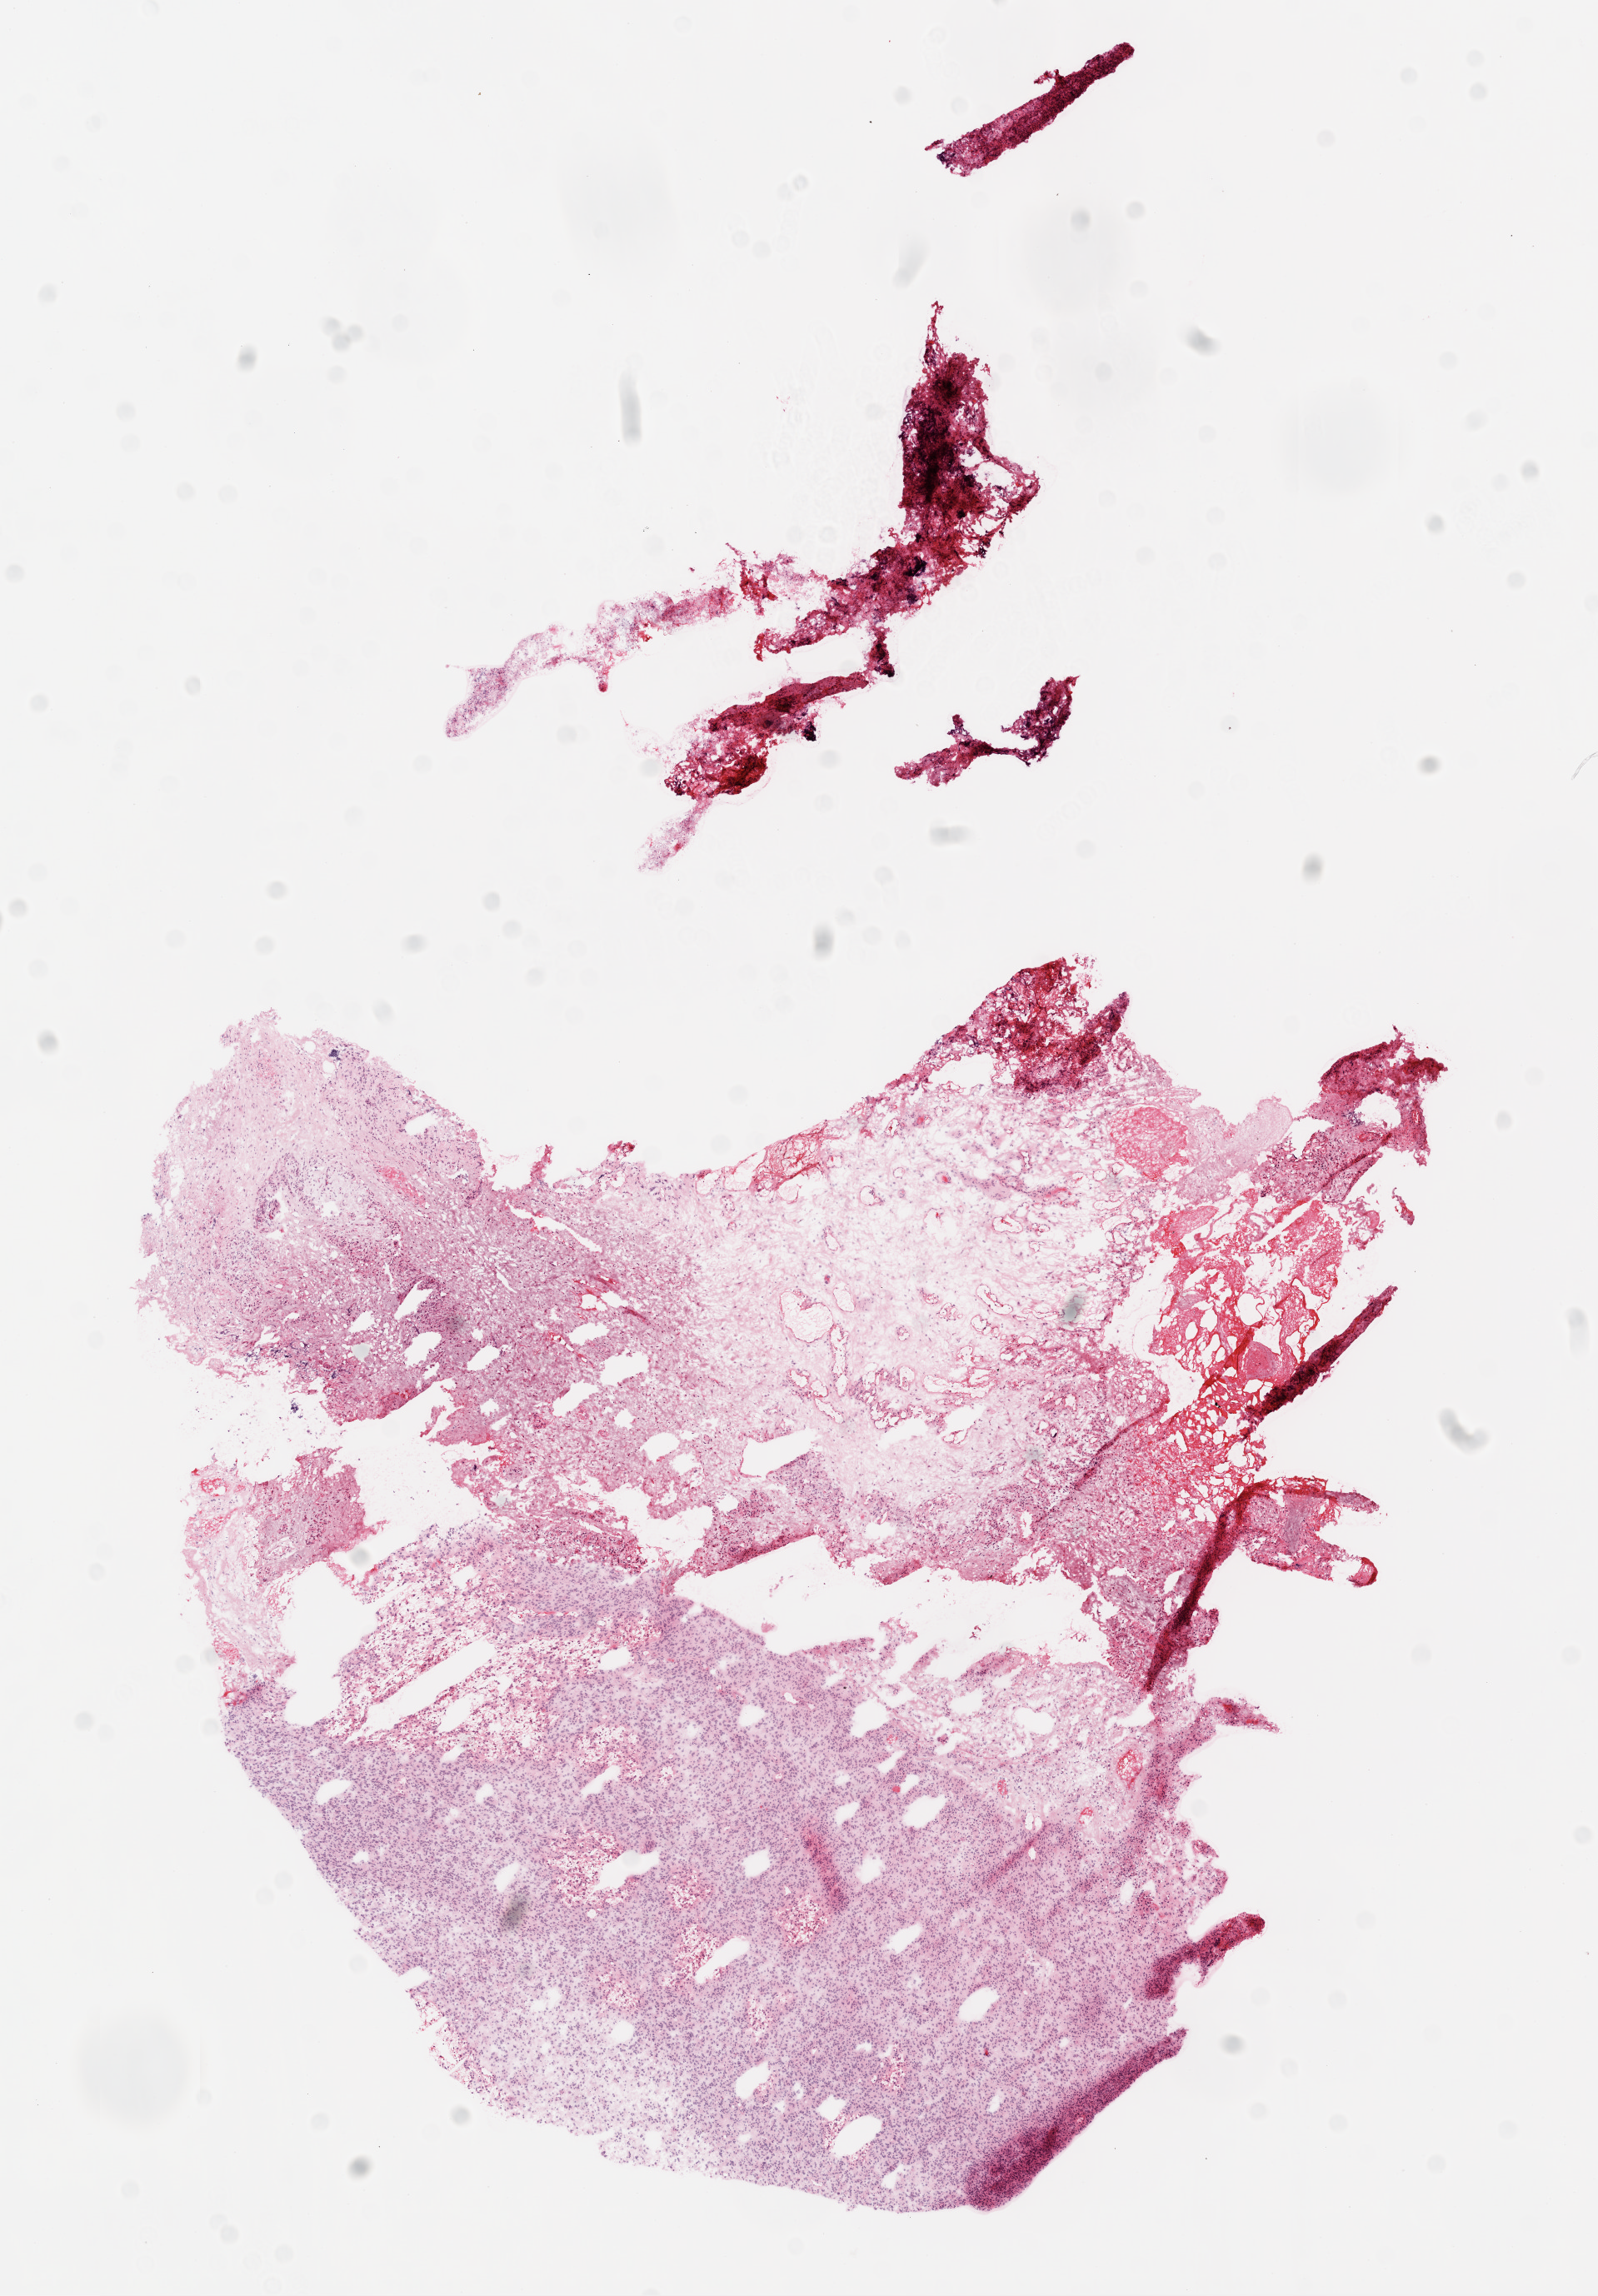
H&E-stained whole-slide image — shown as a low-resolution overview of the whole scanned area (about 7.7 x 11.1 mm, slide scanned at 20x), frozen section from the top of the tissue portion, primary tumour sample from the brain. Female patient; age at initial diagnosis 59 years. Slide review estimates, as recorded: tumour cells 50%, tumour nuclei 85%, normal cells 0%, stromal cells 0%, necrosis 50%.
- histologic diagnosis: Glioblastoma